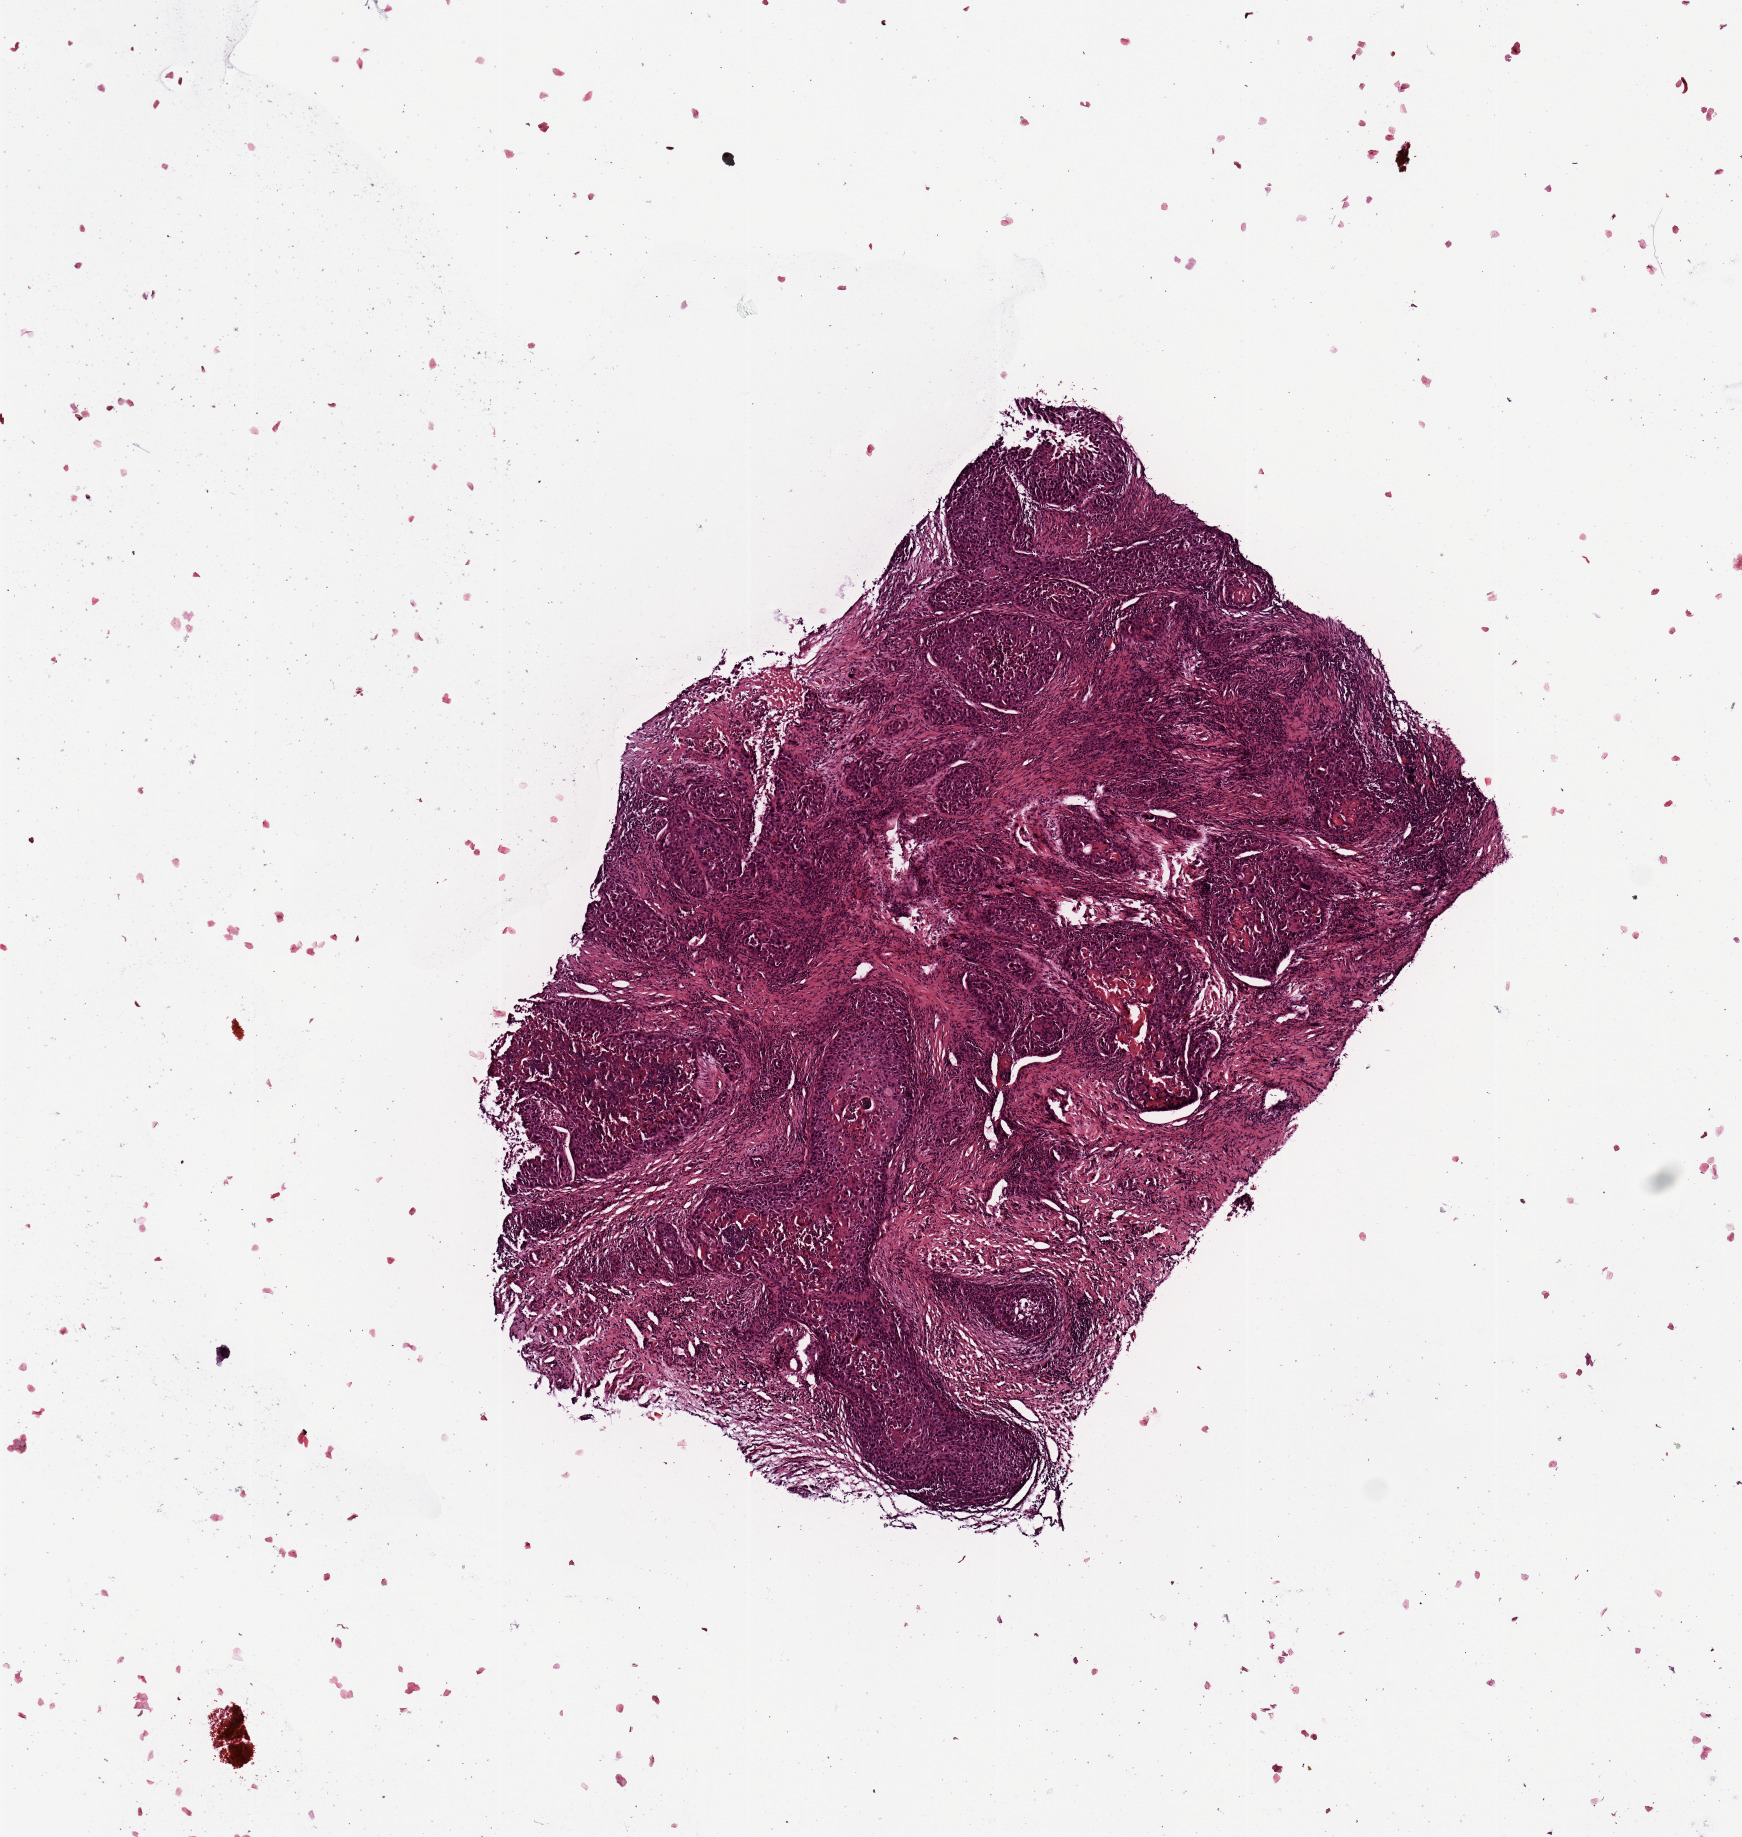
Hematoxylin and eosin (H&E) stained whole-slide image — a low-resolution overview of the entire scanned area, about 6.9 x 7.3 mm, head and neck, tissue type not recorded. Male, 71 y/o.
Patient diagnosis: Squamous cell carcinoma, NOS.